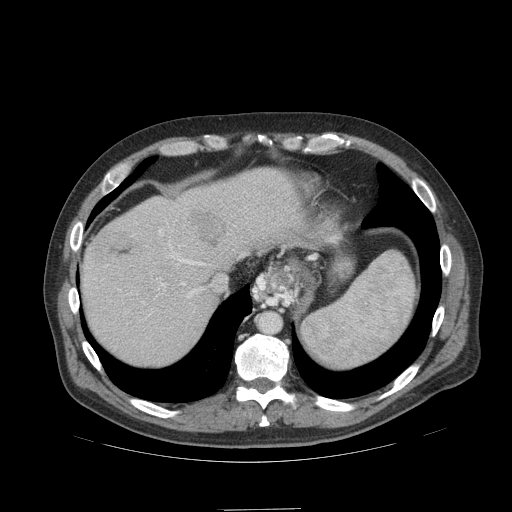
Contrast-enhanced abdominal CT (liver protocol), one axial slice. Position 84 of 99 along the scan axis. Reconstruction kernel STANDARD. 140 kVp. Soft-tissue window (W 400 / L 40 HU). 2.5 mm slice thickness. 512 × 512 image matrix. From the clinical record (not read from this slice): diagnosis: hepatocellular carcinoma (patient treated with transarterial chemoembolisation; whether this scan precedes or follows treatment is not stated here); TNM stage (as recorded): Stage-I; Child-Pugh class: A; tumour nodularity: uninodular; tumour size: 3.6 cm.
Structures marked on this image (semi-automatically segmented with operator editing):
- liver parenchyma outside the tumour (the mass and vessels are separate outlines, so this box may not span the whole liver): bounding box (x1, y1, x2, y2) in pixels: (82, 168, 330, 366)
- mass: (191, 210, 226, 249)
- liver vessels: (159, 223, 205, 298)